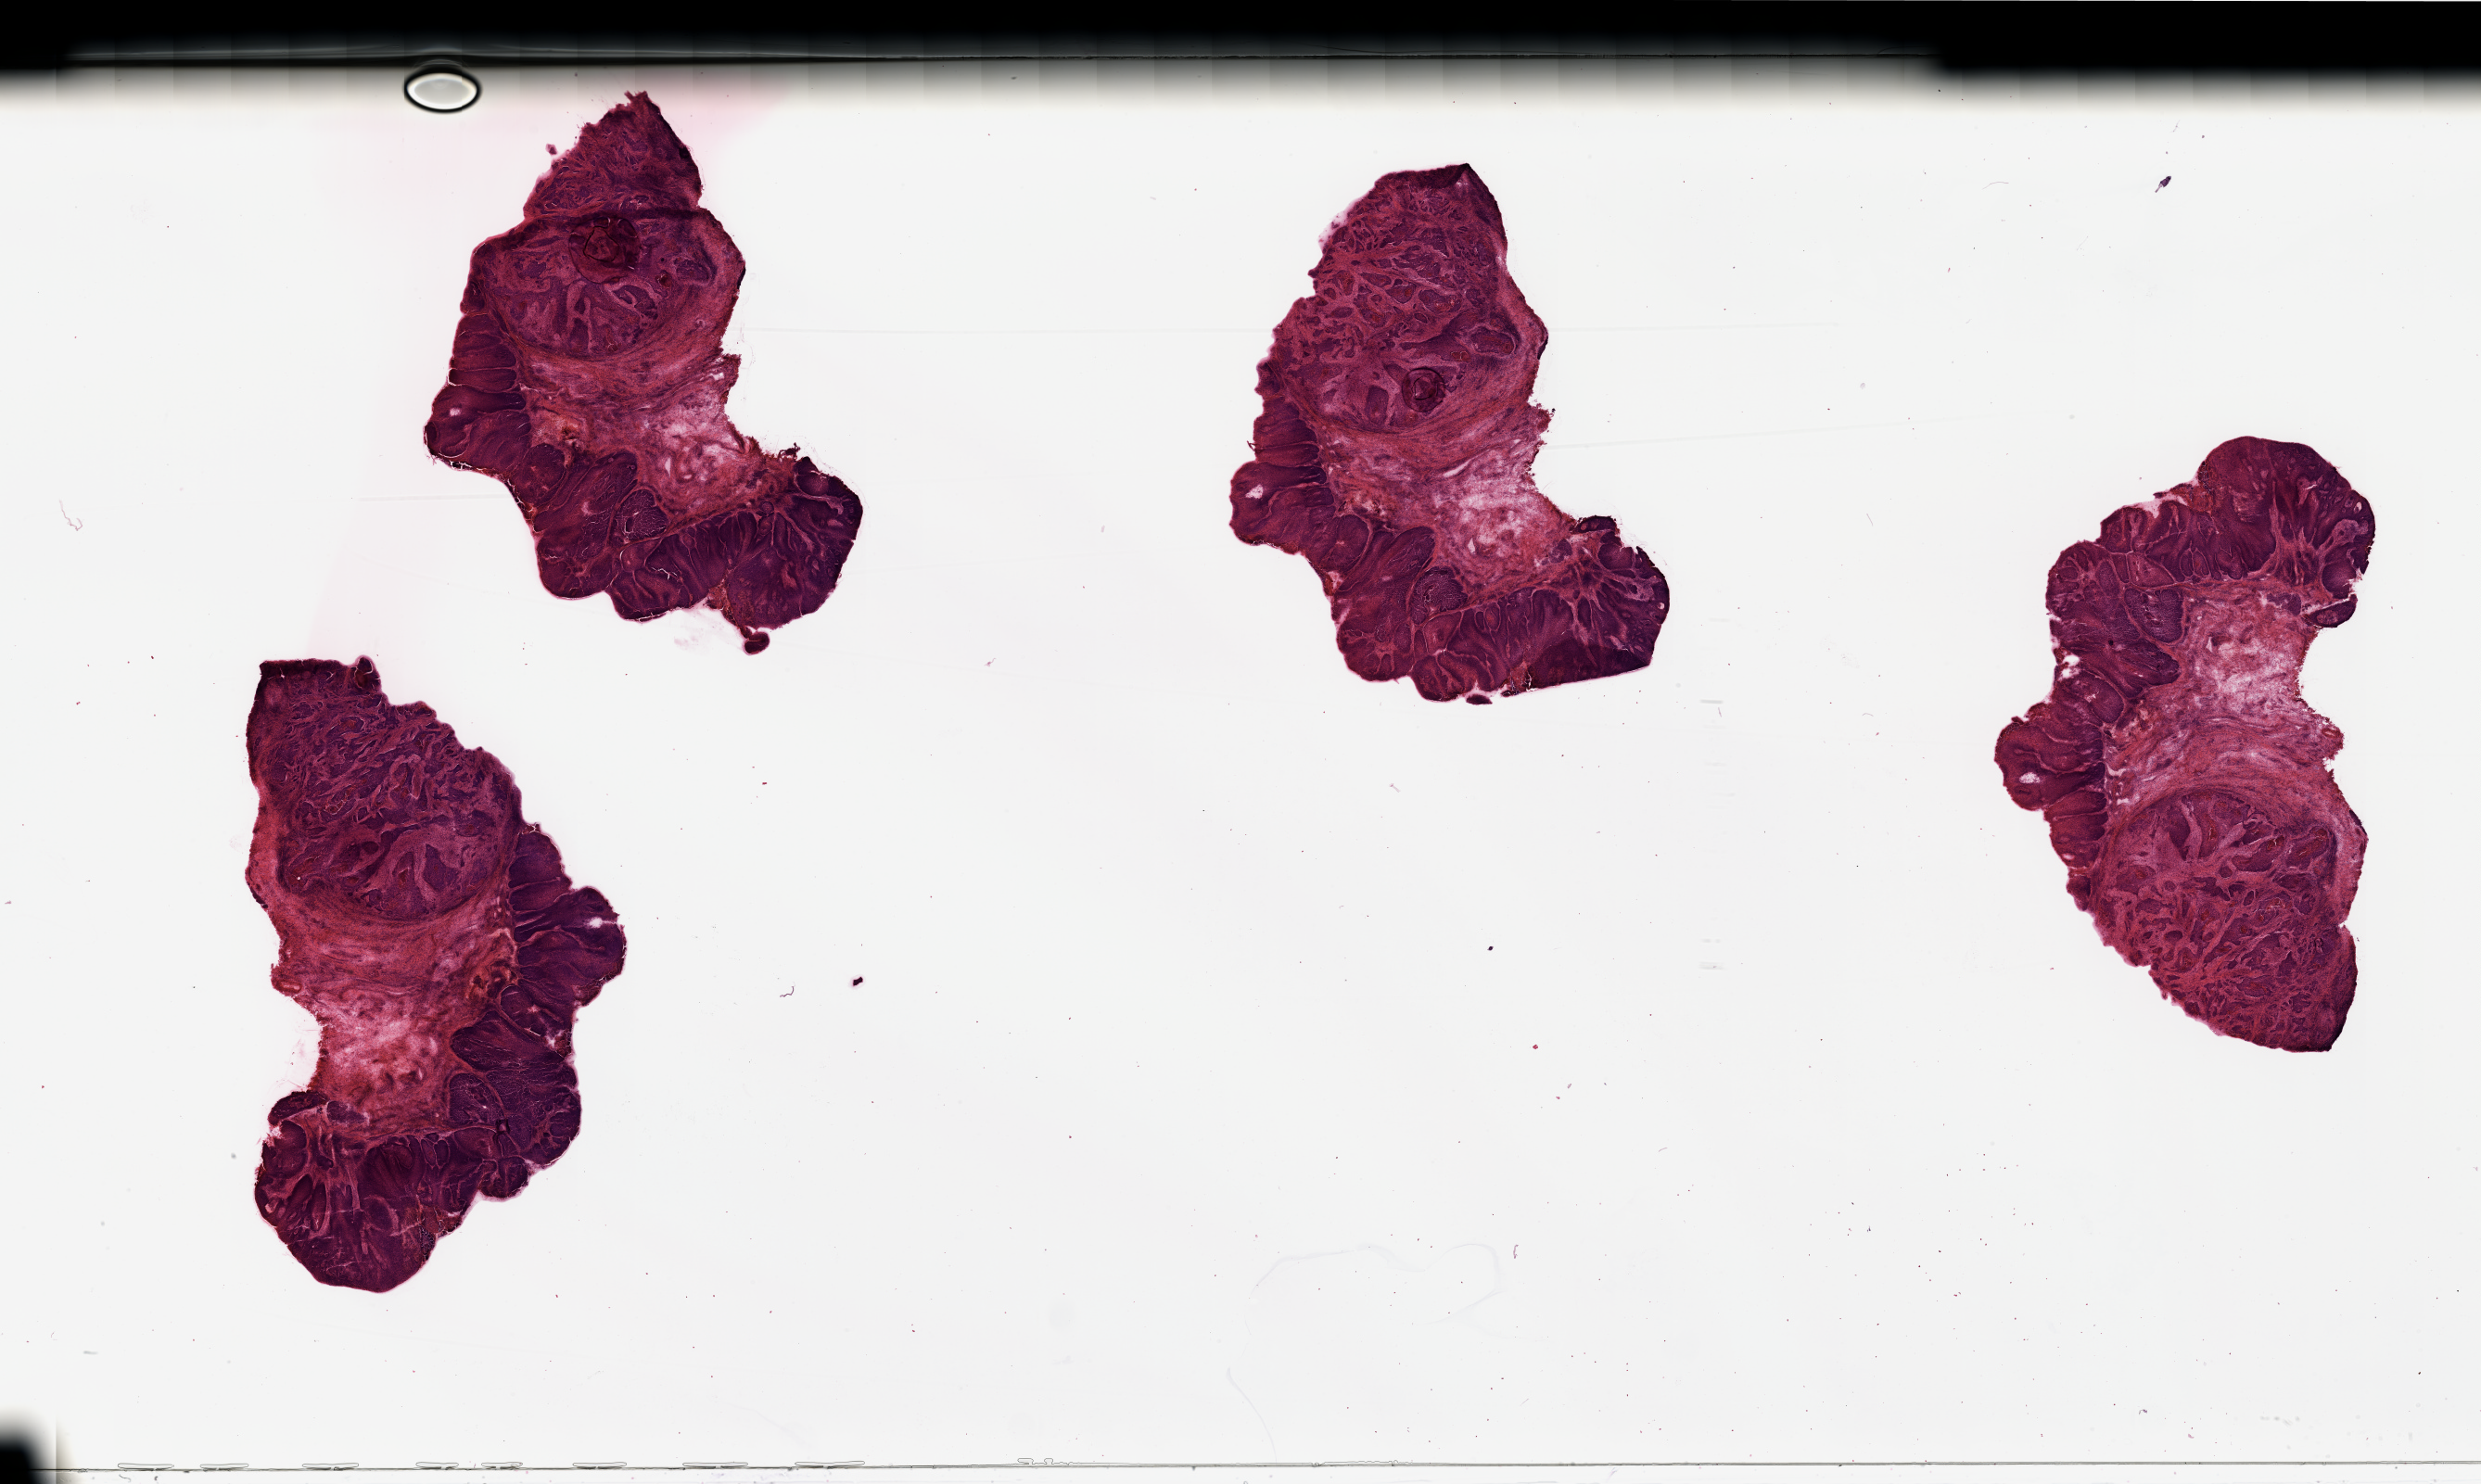
H&E-stained whole-slide image — a low-resolution overview of the entire scanned area, about 42.3 x 25.3 mm (from a 20x scan); head and neck, tissue type not recorded. Male, 63 y/o.
Patient diagnosis: Squamous cell carcinoma, NOS.